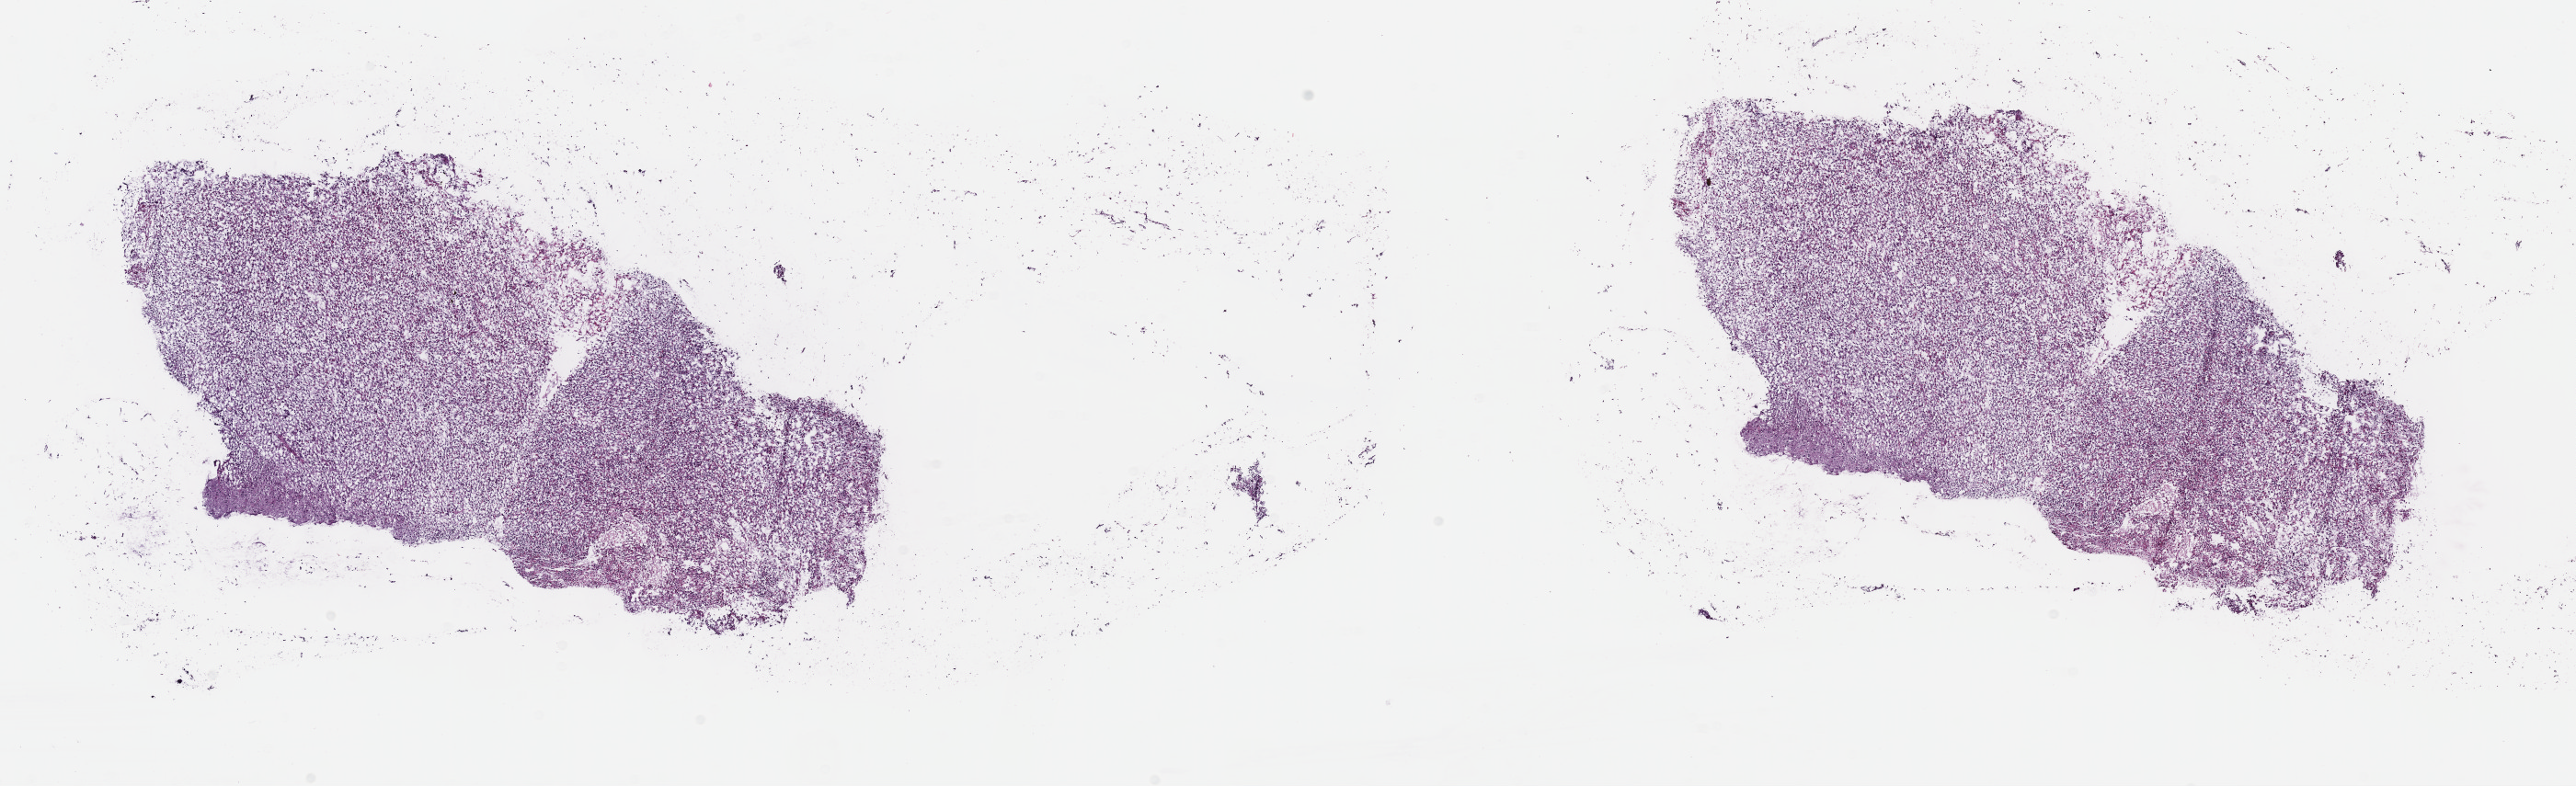
Digitized H&E-stained tissue section (whole slide), a low-resolution overview of the entire scanned area, about 22.7 x 6.9 mm (acquisition: 40x scan). Frozen section from the top of the tissue portion. Brain, primary tumour sample. Patient: male, age at initial diagnosis 71 years. Histologic grade: G3 (poorly differentiated). Pathologist review of this section (percent, as recorded): tumour cells 80%, tumour nuclei 90%, normal cells 5%, stromal cells 15%, necrosis 0%. Inflammatory infiltration, as recorded: lymphocyte infiltration 0%, monocyte infiltration 0%, neutrophil infiltration 0%.
Pathologic diagnosis: Oligodendroglioma, anaplastic (cerebrum).